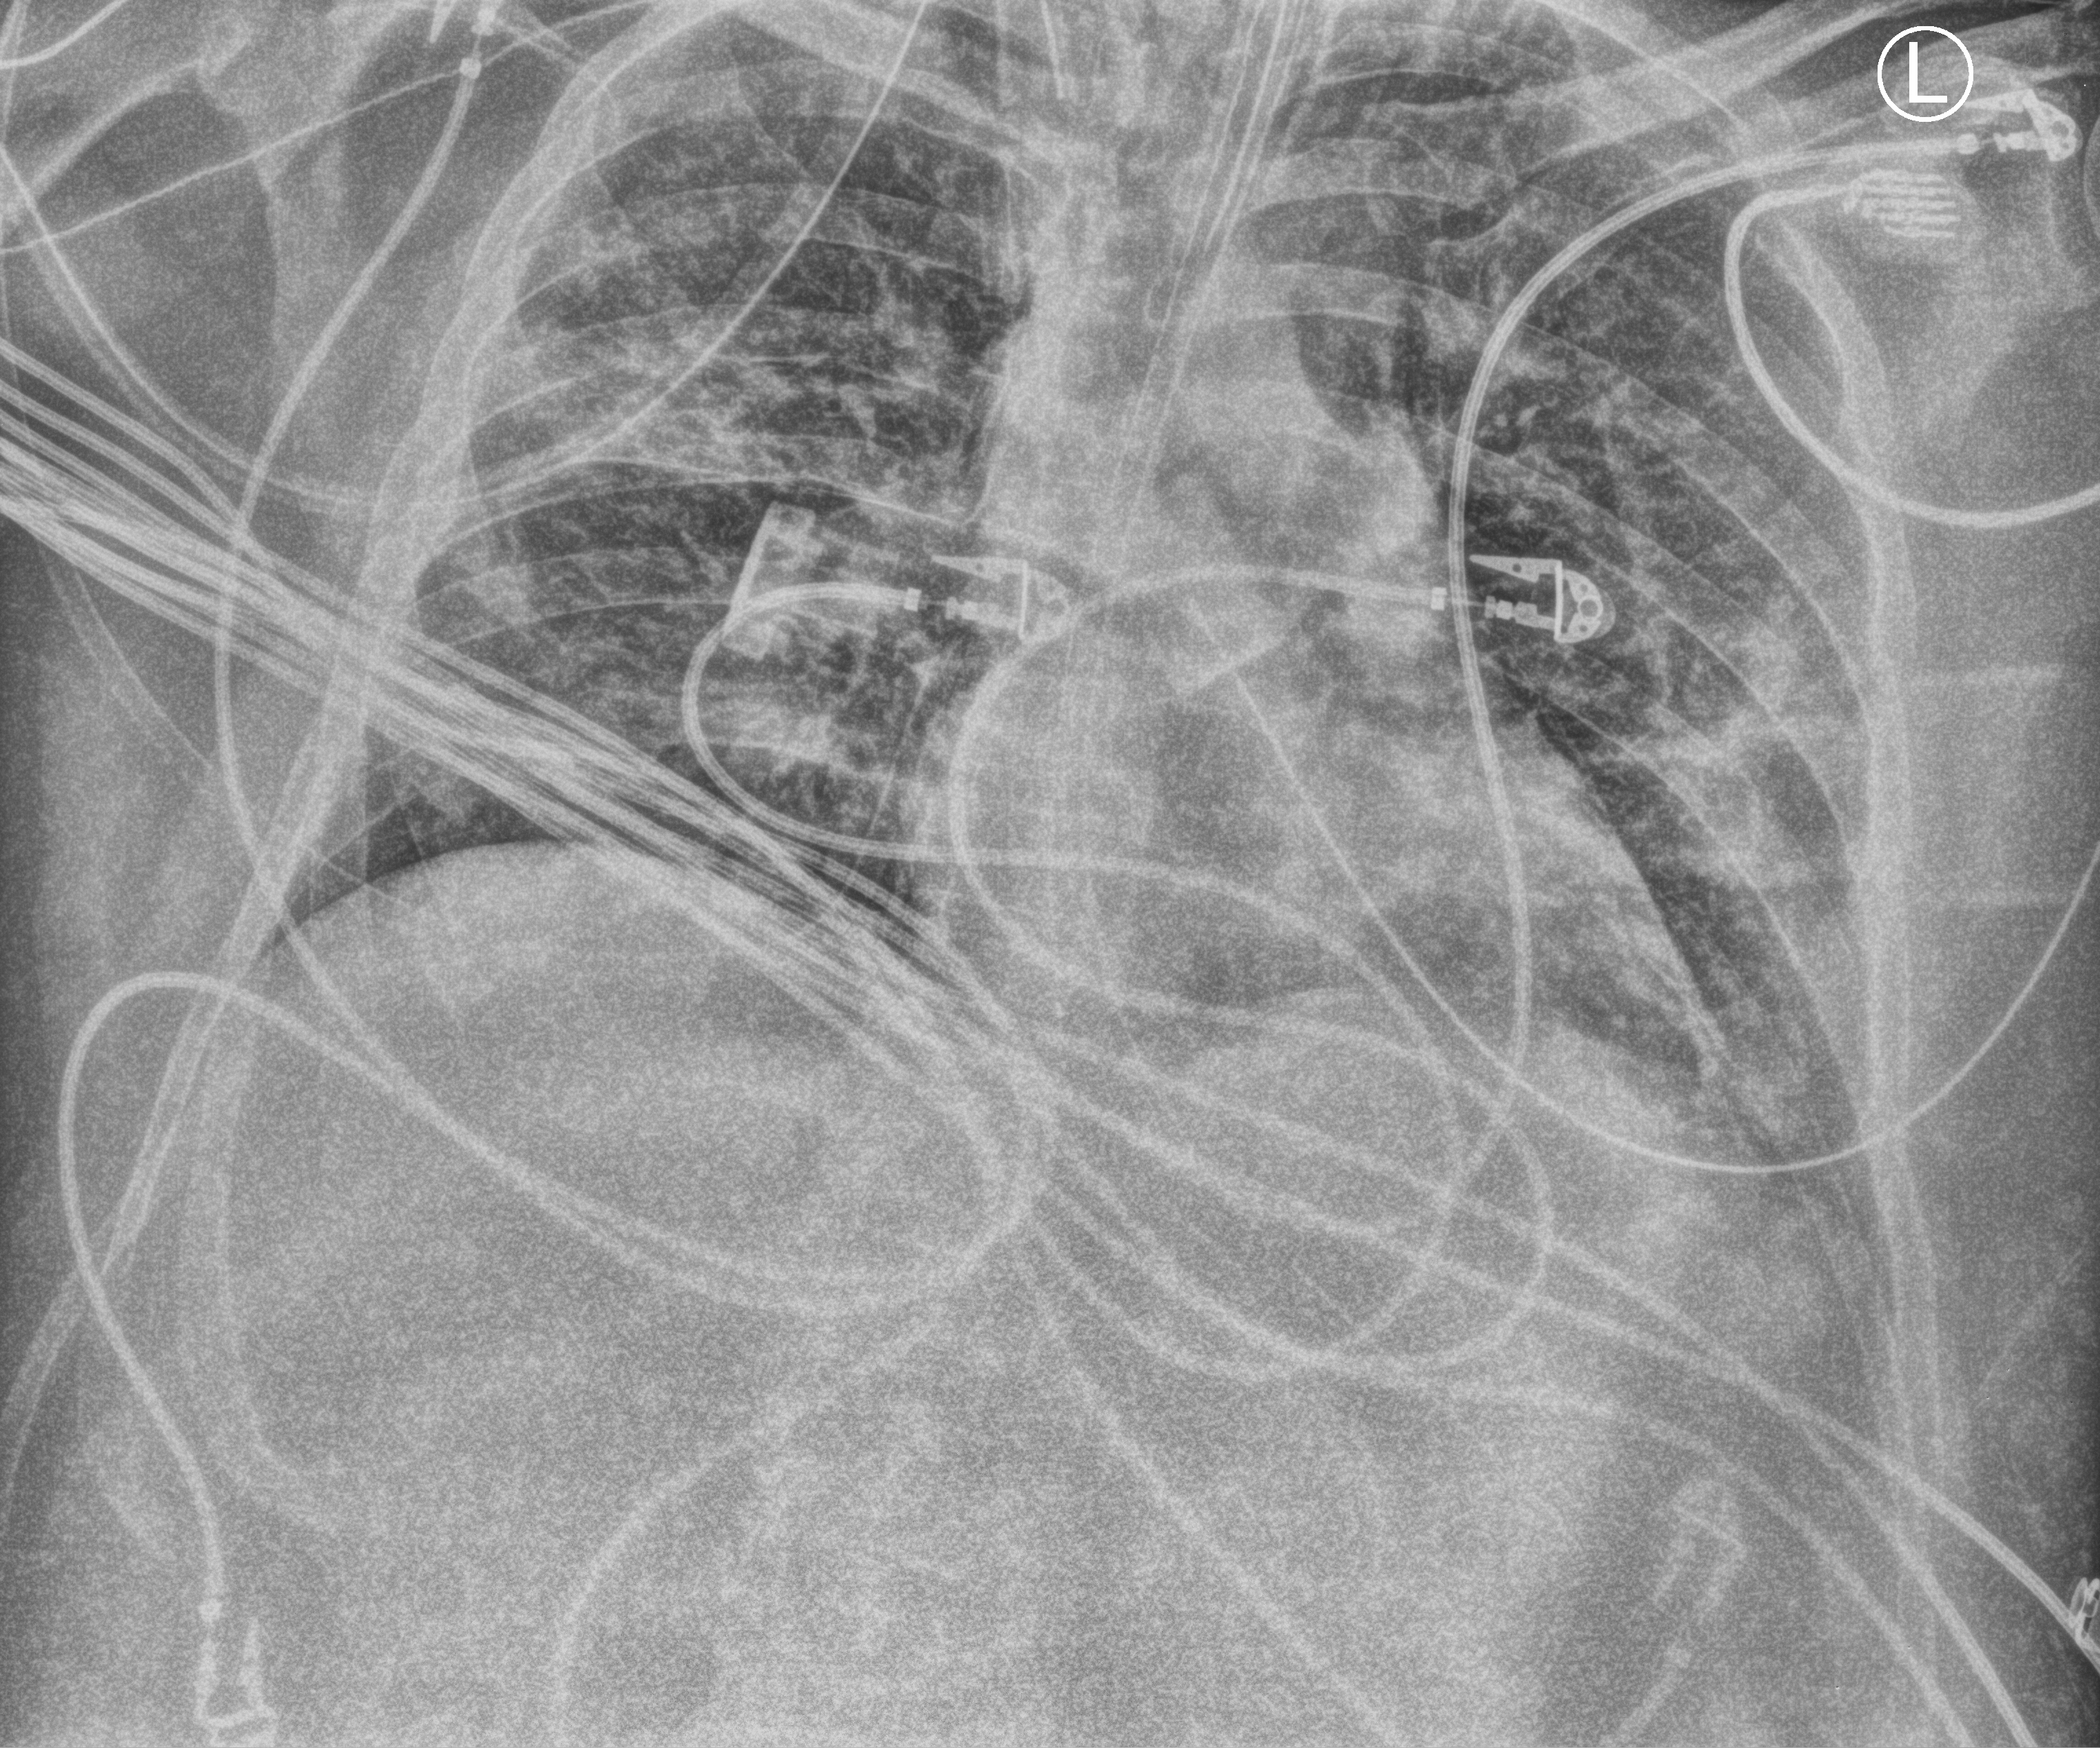
Chest X-ray (portable); anteroposterior (AP) projection. Adult patient hospitalised with COVID-19, age 18–59 years.
From the hospital-stay record, not from the radiograph (when in the stay this image was taken is not recorded):
- hypertension (admission record): yes